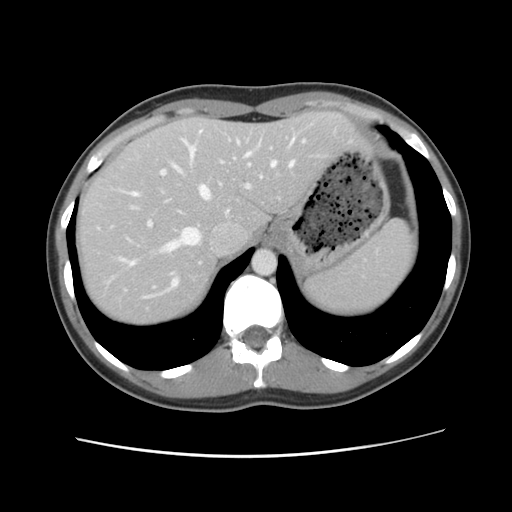
Contrast-enhanced abdominal CT, one axial slice; position 91 of 134 along the scan axis; 120 kVp; intravenous contrast given; soft-tissue window (W 400 / L 40 HU); 2.5 mm slice thickness; 512 × 512 image matrix. Female patient, age 33 years. Case-level facts recorded for this patient, not image findings: diagnosis: colorectal cancer liver metastases, imaged before liver resection.
Structures marked on this image (expert manual segmentation):
- hepatic veins: bounding box (x1, y1, x2, y2) in pixels: (124, 131, 305, 288)
- liver: (76, 112, 364, 326)
- planned liver remnant (the part of the liver to remain after resection): (76, 113, 364, 326)
- portal vein (with intrahepatic branches): (129, 139, 273, 229)